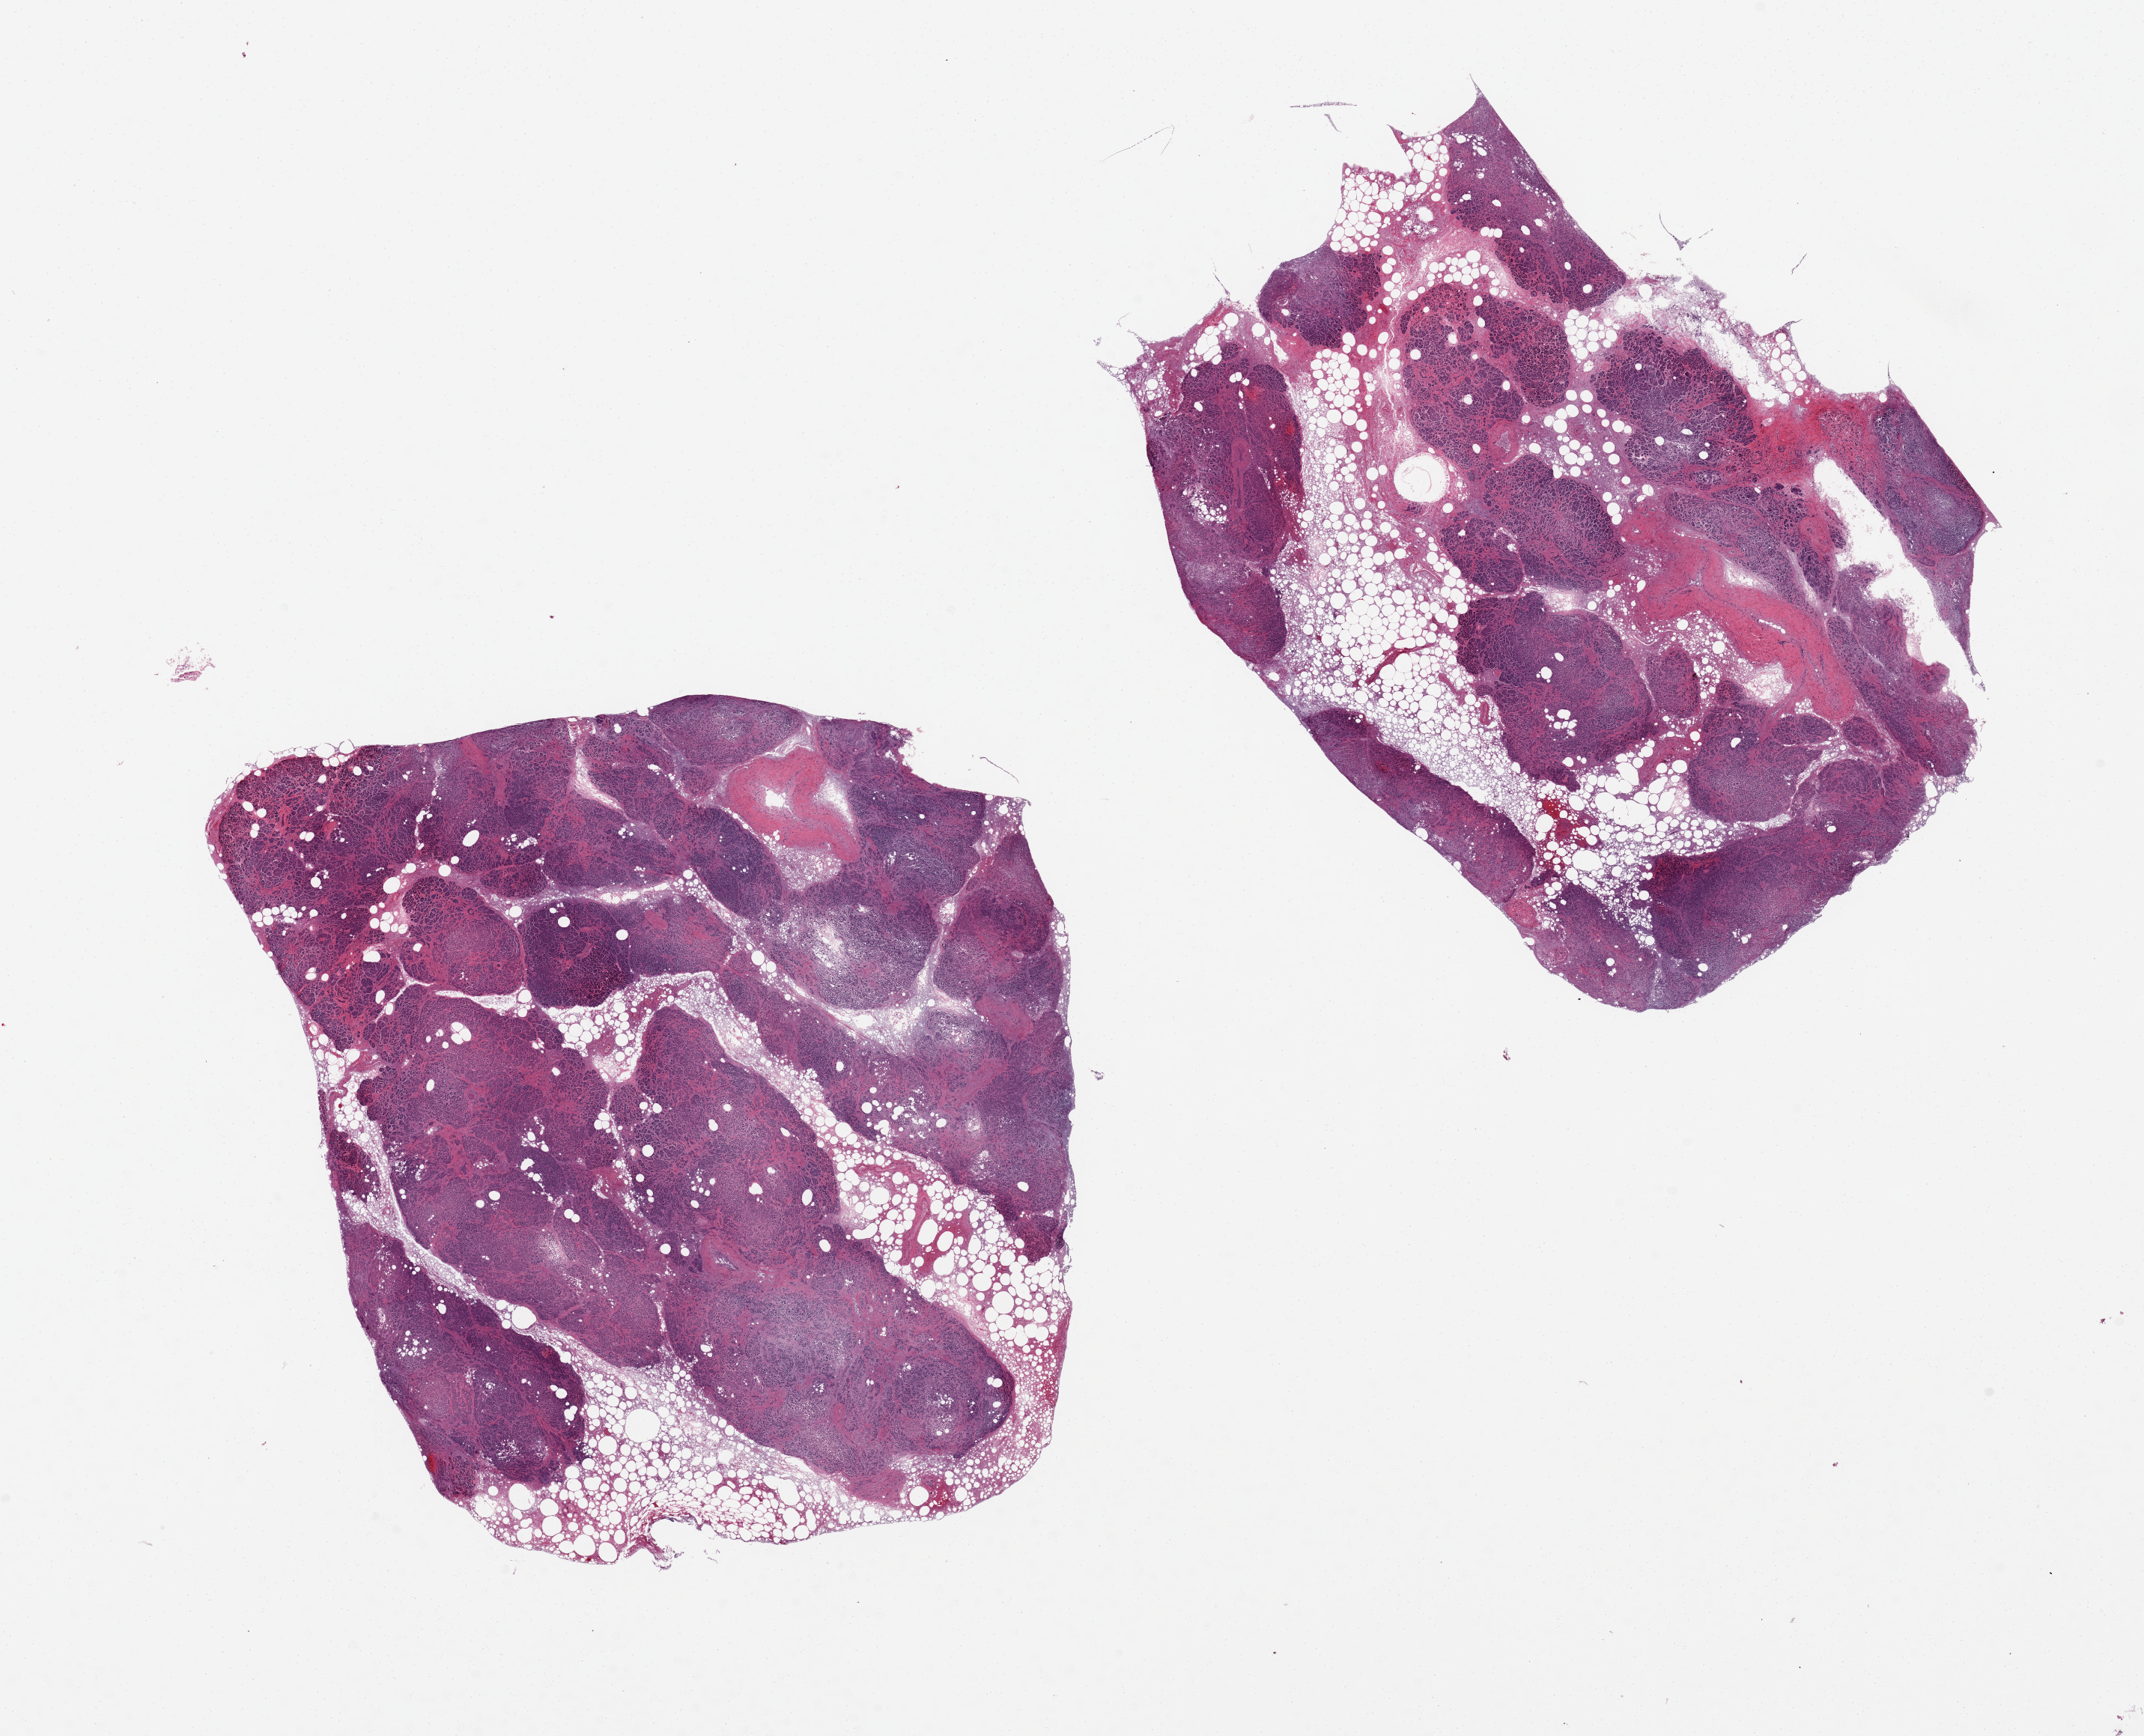
Whole-slide image, haematoxylin and eosin stain — shown as a low-resolution overview of the whole scanned area (about 22.6 x 18.3 mm), PAXgene-fixed paraffin-embedded (PFPE) section, sampled site (target tissue): pancreas, tissue donor sample.
Reviewer comment on this tissue sample: 2 pieces marked autolysis and saponification.